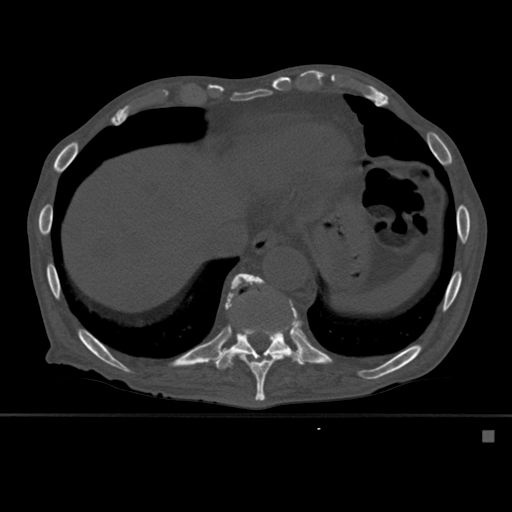
CT including the spine, one axial slice. Position 306 of 527 along the scan axis. Bone window (W 1800 / L 400 HU). 1.5 mm slice thickness. 512 × 512 image matrix, field of view 373 × 373 mm. Patient: male, 78 years. Case-level facts recorded for this patient, not image findings: primary cancer: prostate.
Outlined on this slice (semi-automatically segmented with operator editing):
- T10 vertebra: bounding box <225,273,301,401> (left, top, right, bottom; pixels)
- T11 vertebra: <213,292,306,370>